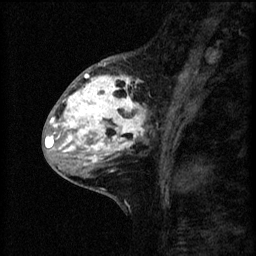
Breast MRI (dynamic contrast-enhanced), one sagittal slice; slice 25 of 60 in the series (ordered by position); 3 images stored at this slice position (order not interpretable as contrast timing); 1.5 T; TE 4.2 ms, TR 8.2 ms; 2 mm slice thickness; 256 × 256 image matrix, field of view 180 × 180 mm. Female patient, age 41 years.
Annotated regions visible in this slice (semi-automatically segmented with operator editing):
- analysis volume of interest (the breast-tissue region the enhancement analysis was run in; not a lesion): bounding box [x1, y1, x2, y2] px = [53, 62, 155, 175]
- tumour enhancement mask (voxels above the 70 % enhancement threshold inside the analysis volume of interest): [53, 64, 146, 163]